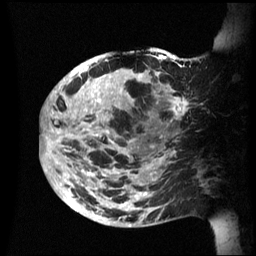
Breast MRI (dynamic contrast-enhanced), one sagittal slice; slice 22 of 60 in the series (ordered by position); dynamic contrast-enhanced series, image 2 of 3 at this slice position (ordered by acquisition); 1.5 T; TE 4.2 ms, TR 8.4 ms; 2.4 mm slice thickness; 256 × 256 image matrix. Female patient, age 48 years.
Structures marked on this image (semi-automatically segmented with operator editing):
- analysis volume of interest (the breast-tissue region the enhancement analysis was run in; not a lesion): bounding box [x1, y1, x2, y2] px = [42, 47, 202, 227]
- tumour enhancement mask (voxels above the 70 % enhancement threshold inside the analysis volume of interest): [42, 54, 191, 227]